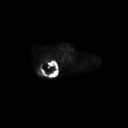
FDG PET of an extremity soft-tissue mass (from a PET/CT study), one axial slice; position 213 of 267 along the scan axis; 3.27 mm slice thickness; 128 × 128 image matrix, field of view 700 × 700 mm. Male patient, age 61 years. Case-level facts recorded for this patient, not image findings: histological type: pleiomorphic spindle cell undifferentiated; grade: high; site of the primary tumour: right parascapusular.
Annotated regions visible in this slice (expert contour drawn on MRI and transferred to this co-registered scan by the dataset authors):
- gross tumour volume including surrounding oedema: bounding box (x1, y1, x2, y2) in pixels: (37, 60, 60, 76)
- gross tumour volume (mass): (41, 60, 57, 75)